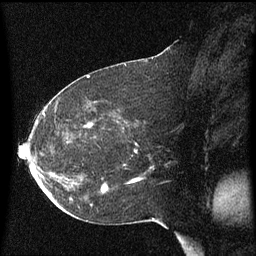
Breast MRI (dynamic contrast-enhanced), one sagittal slice; position 31 of 60 along the scan axis; dynamic contrast-enhanced series, image 2 of 3 at this slice position (ordered by acquisition); 1.5 T; TE 4.2 ms, TR 8.4 ms; 2 mm slice thickness; 256 × 256 image matrix. Patient: female, 54 years. From the clinical record (not read from this slice): setting: breast cancer imaged before/during neoadjuvant chemotherapy; receptor status: HR-positive, HER2-negative.
Annotated regions visible in this slice (semi-automatic segmentation, software-assisted and operator-edited):
- analysis volume of interest (the breast-tissue region the enhancement analysis was run in; not a lesion): box from (x=102, y=166) to (x=154, y=191) px
- tumour enhancement mask (voxels above the 70 % enhancement threshold inside the analysis volume of interest): (x=103, y=186)–(x=108, y=191)